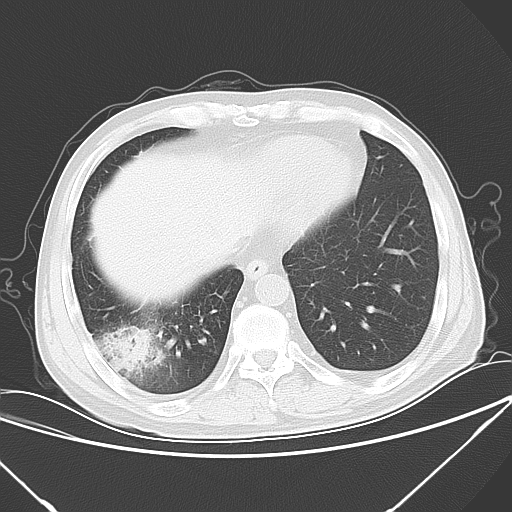
Chest CT, one axial slice. Position 18 of 57 along the scan axis. Lung window (W 1500 / L -600 HU). 5 mm slice thickness. 512 × 512 image matrix. Male patient, age 54 years. From the clinical record (not read from this slice): clinical TNM (as recorded): T2 N1 M0; histopathological grade: G3.
Structures marked on this image (bounding box drawn by a radiologist):
- lung tumour (recorded histology: adenocarcinoma): bounding box <103,323,155,374> (left, top, right, bottom; pixels)